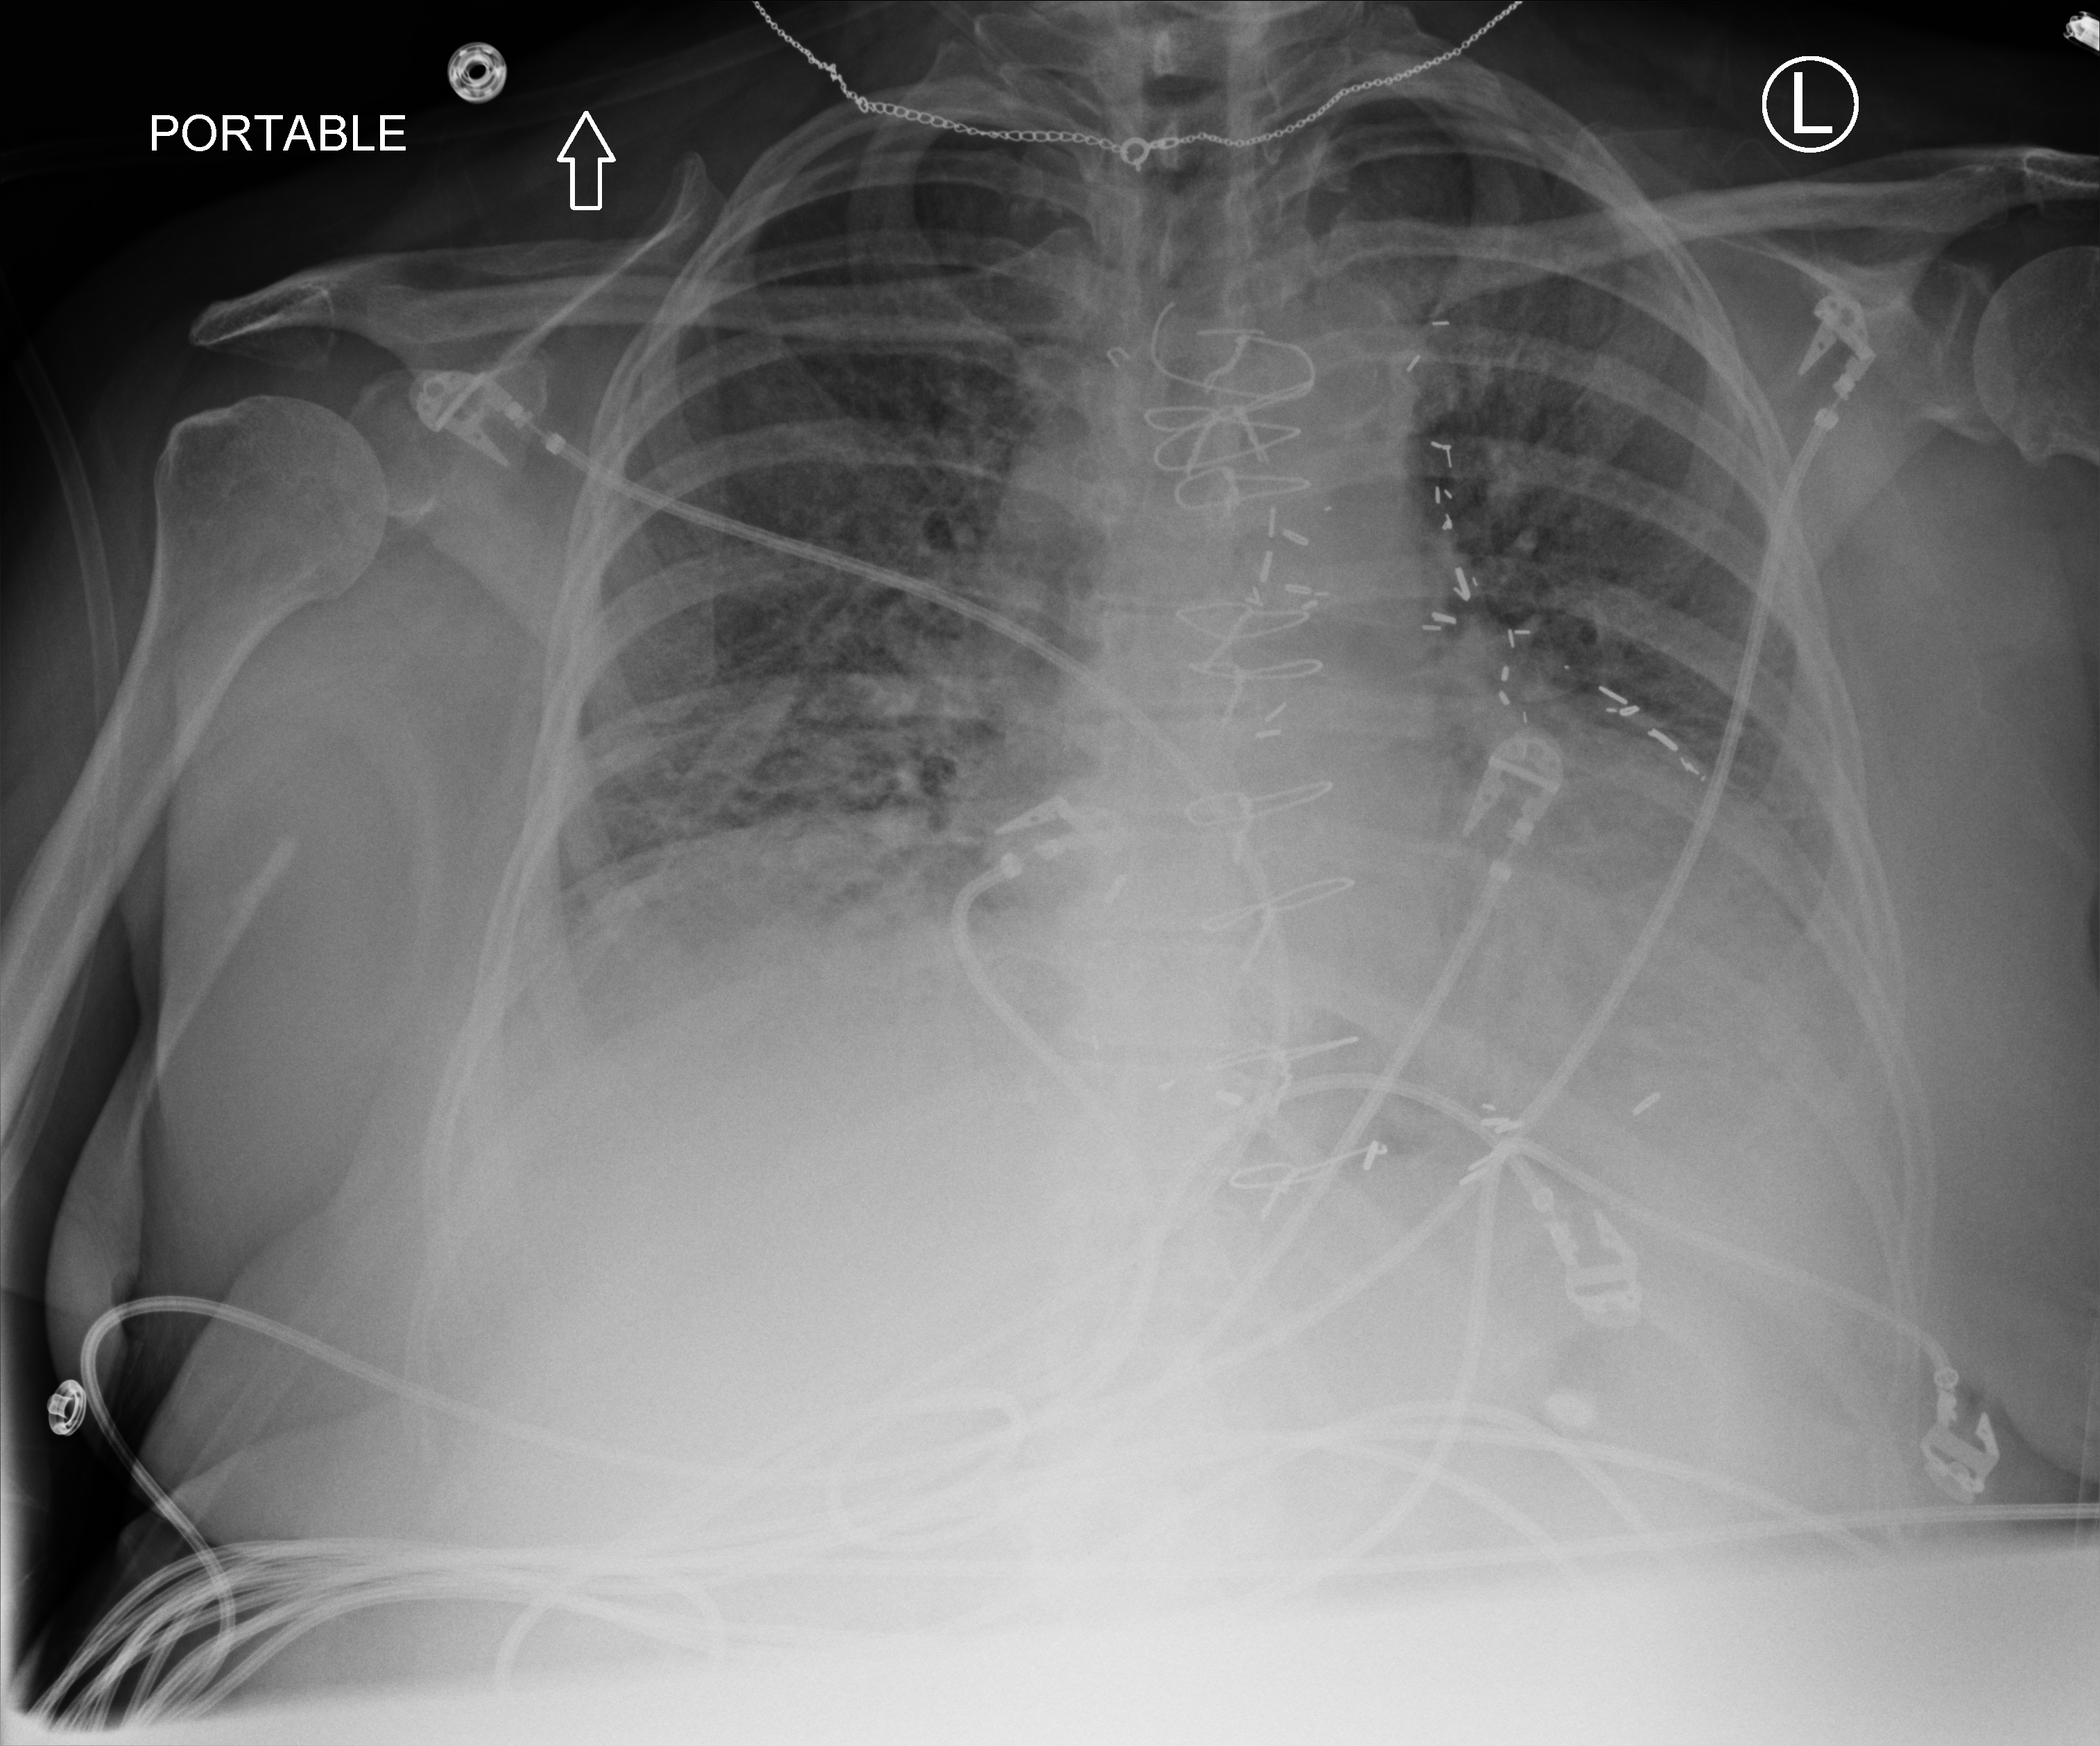
Chest X-ray (portable), anteroposterior (AP) projection. Patient hospitalised with COVID-19; female, aged 60–74 years.
Admission-level facts for this patient (not findings on this image; timing relative to this image not recorded): admitted to intensive care during this hospital stay: yes.